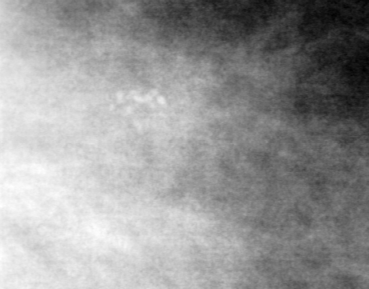
Region of interest cut from a scanned film mammogram (one marked finding), right breast, CC view.
Calcifications, morphology pleomorphic, distribution clustered; BI-RADS assessment category 4; pathology result (as recorded, not read from the image): benign.